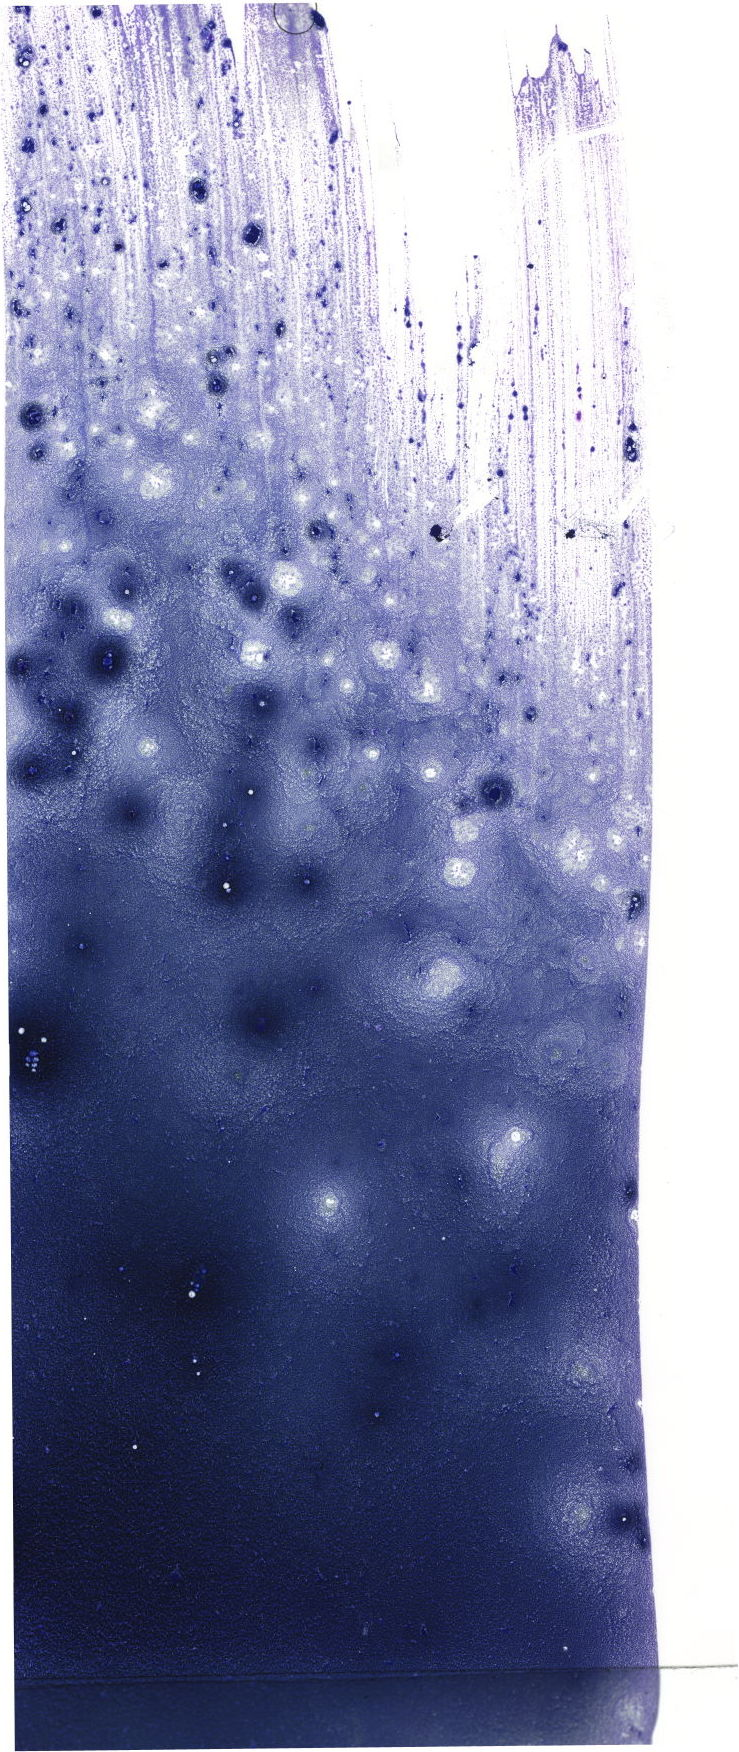
Bone marrow aspirate smear, May-Grünwald-Giemsa (MGG) stain, whole-slide image — a low-resolution overview of the entire scanned area, about 20.9 x 49.7 mm. Patient sex: female.
Diagnosis: Chronic Phase Chronic Myeloid Leukemia, BCR-ABL1 Positive.